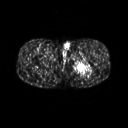
FDG PET of an extremity soft-tissue mass (from a PET/CT study), one axial slice. Slice 250 of 267 in the series (ordered by position). 128 × 128 image matrix, field of view 500 × 500 mm. Male patient, age 27 years. Case-level facts recorded for this patient, not image findings: histological type: extraskeletal osteosarcoma; grade: high; site of the primary tumour: left adductur.
Annotated regions visible in this slice (expert contour drawn on MRI and transferred to this co-registered scan by the dataset authors):
- gross tumour volume (mass): bounding box (x1, y1, x2, y2) in pixels: (71, 56, 95, 74)